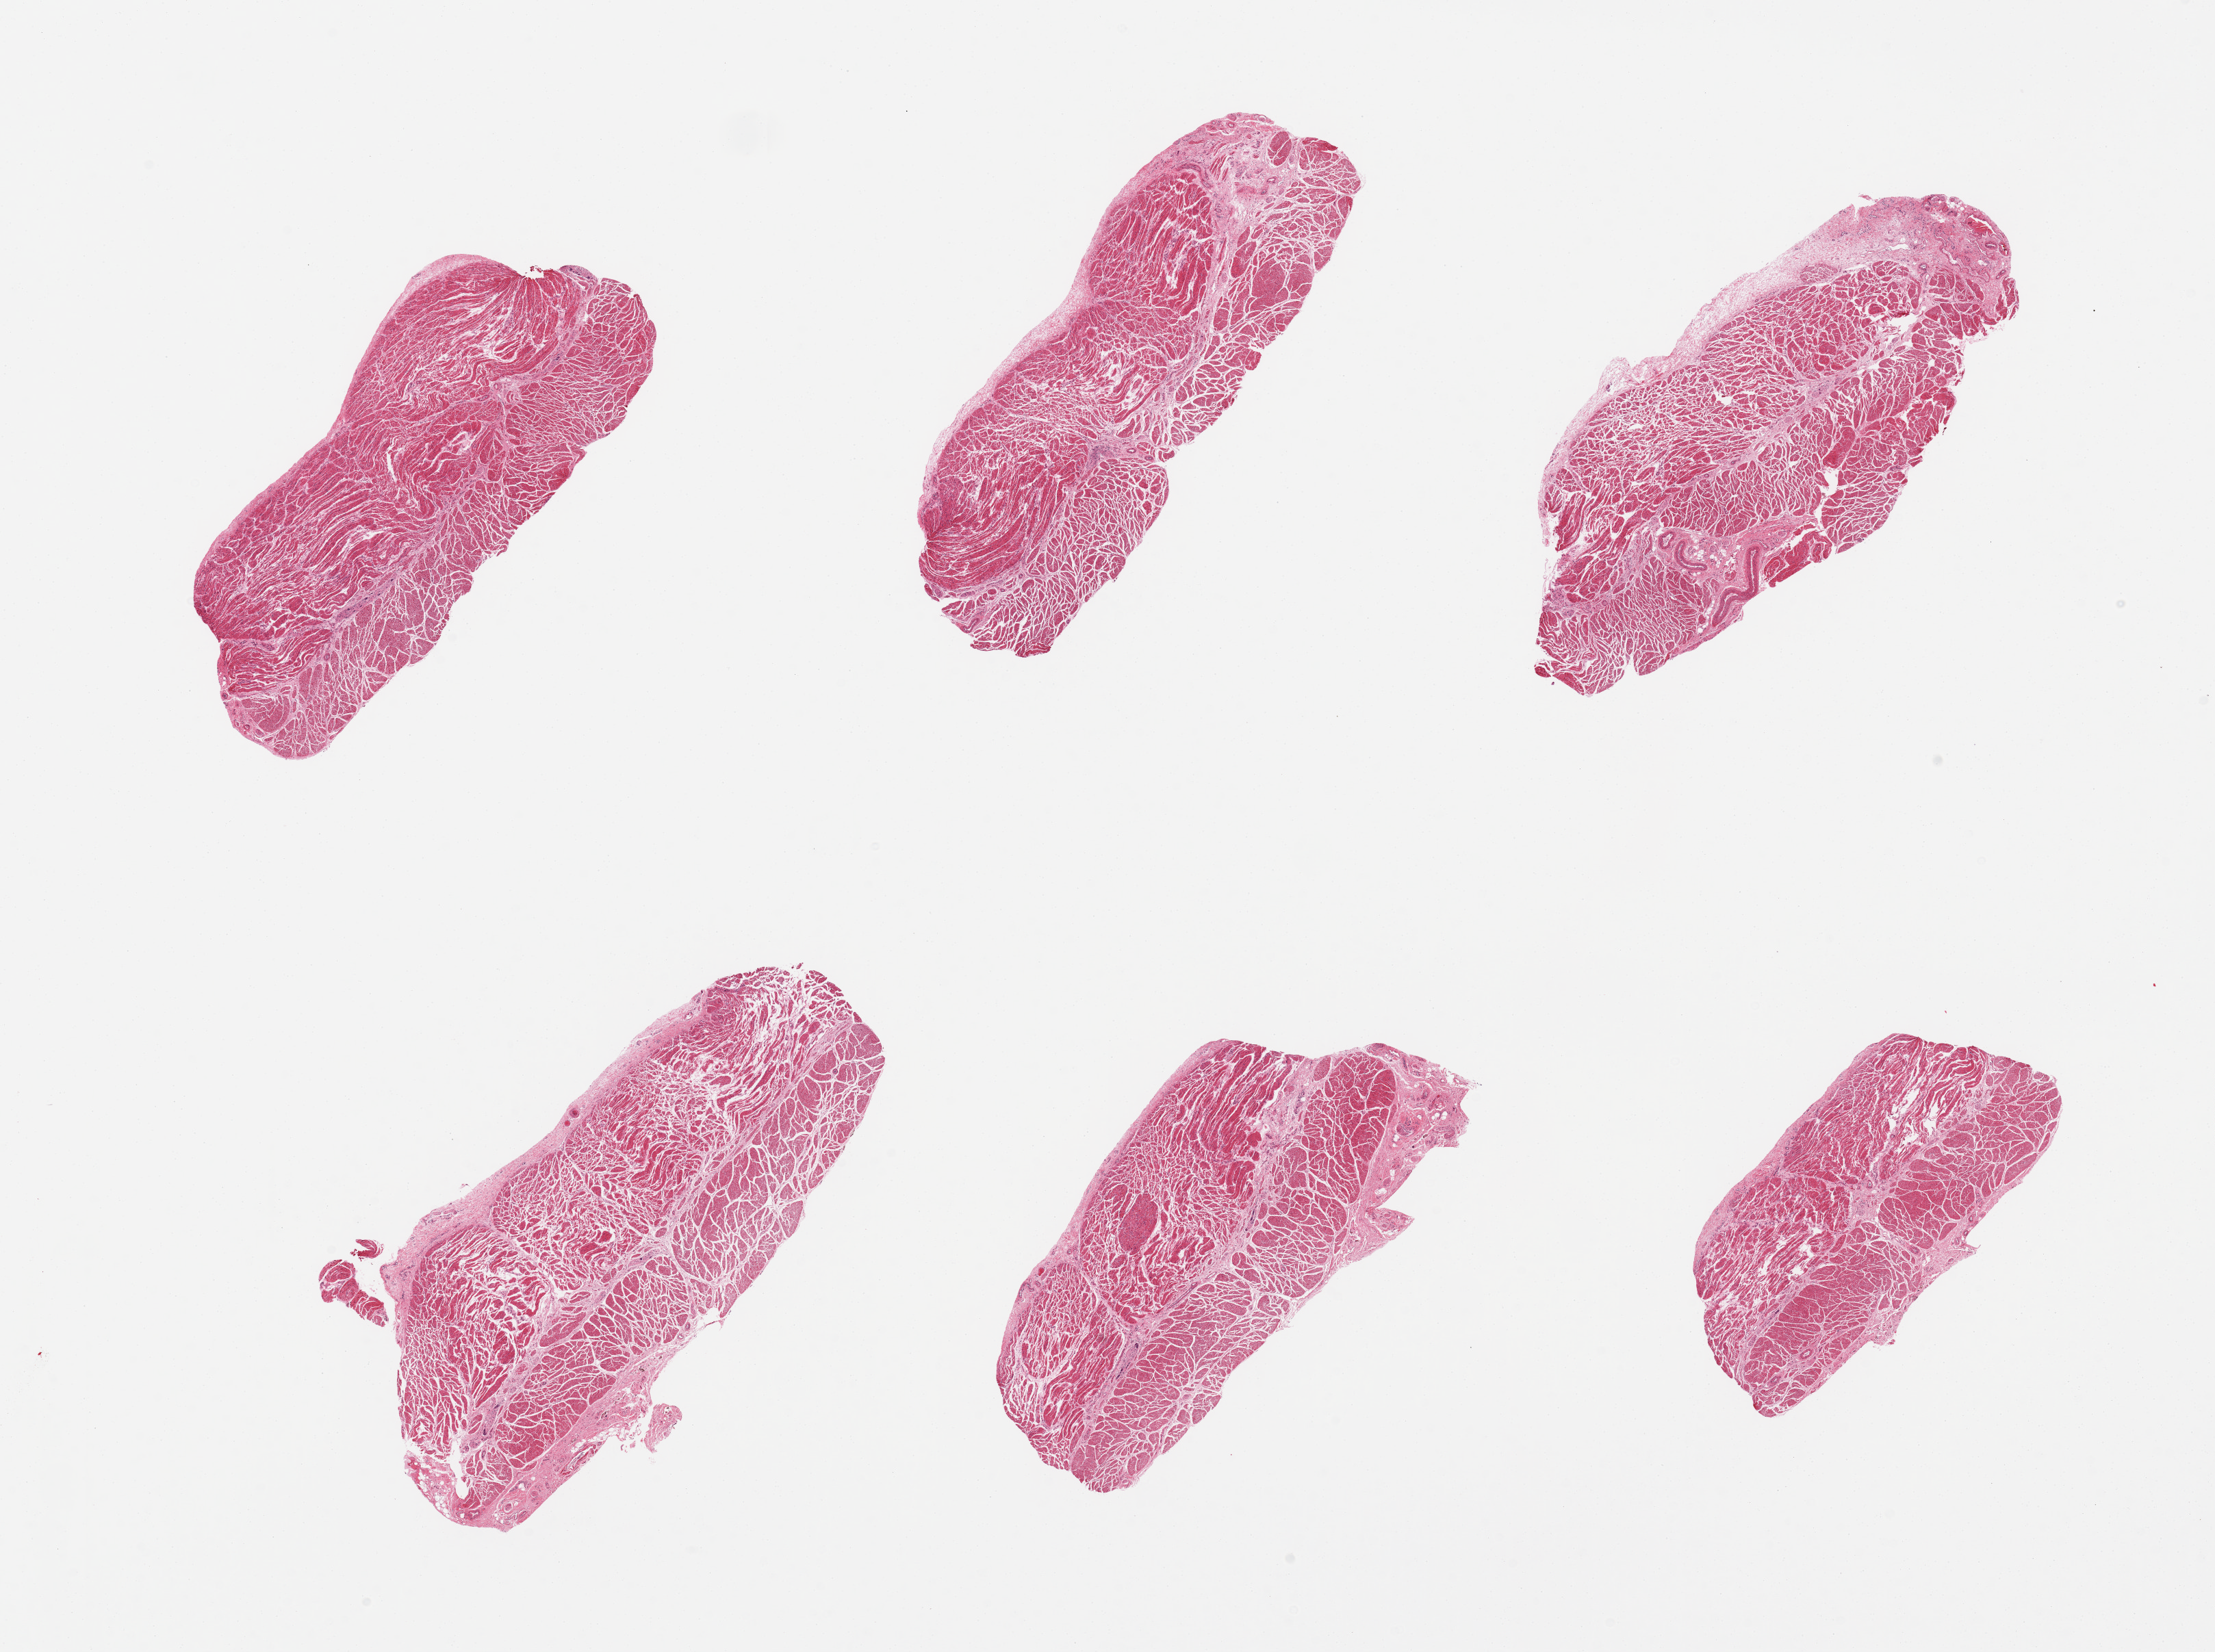
Whole-slide image, H&E stain, brightfield, a low-resolution overview of the entire scanned area, about 25.6 x 19.1 mm (slide scanned at 20x); PAXgene-fixed paraffin-embedded (PFPE) section; sampled site (target tissue): esophageal muscle; tissue donor sample. Male donor.
Review note (as recorded): 6 pieces, all muscularis, good specimens.